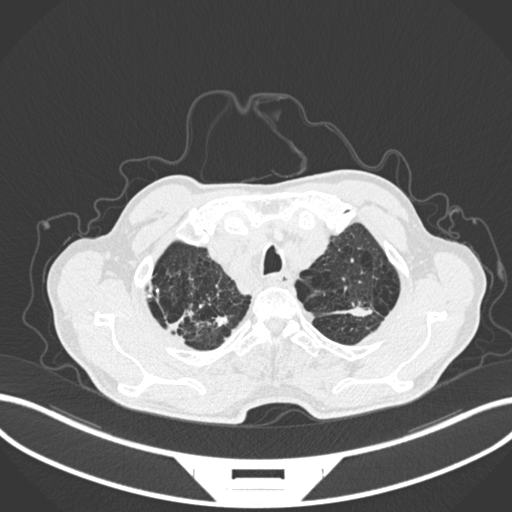
Chest CT, one axial slice. Position 244 of 287 along the scan axis. Reconstruction kernel B30f. Lung window (W 1500 / L -600 HU). 1 mm slice thickness. 512 × 512 image matrix, field of view 400 × 400 mm. Male patient, age 74 years. From the clinical record (not read from this slice): clinical TNM (as recorded): T2a N1 M0.
Annotated regions visible in this slice (rectangle marked by the reading radiologist):
- lung tumour (recorded histology: adenocarcinoma): box from (x=334, y=305) to (x=379, y=320) px